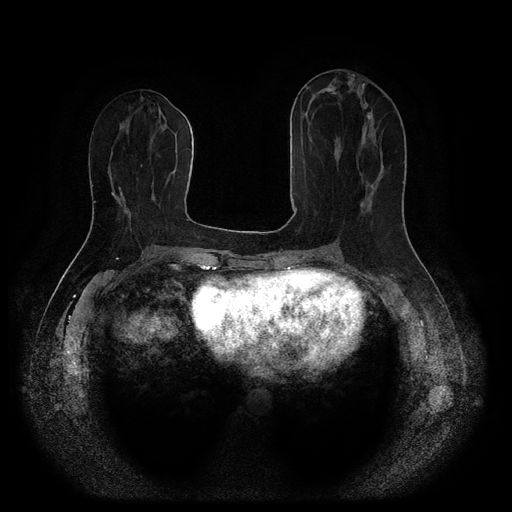
Breast MRI (dynamic contrast-enhanced, multi-phase), one axial slice; position 42 of 116 along the scan axis; dynamic contrast-enhanced series, time point 2 of 5 at this slice position (early post-contrast); 1.5 T; TE 2.6 ms, TR 5.3 ms; 2.2 mm slice thickness; 512 × 512 image matrix, field of view 360 × 360 mm. Female patient, age 53 years.
Annotated regions visible in this slice (semi-automatically segmented with operator editing):
- breast lesion (labelled 'tumour' in the annotation; benign lesions carry a separate 'benign' label): bounding box [x1, y1, x2, y2] px = [364, 103, 373, 119]